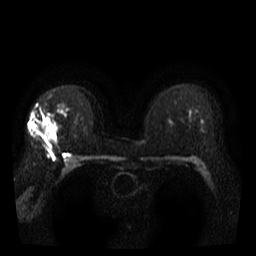
Breast MRI, one axial slice. Diffusion-weighted series; image 2 of 4 stored at this slice position (different b-values; order by instance number). 3 T. 5 mm slice thickness. 256 × 256 image matrix, field of view 300 × 300 mm. Female patient.
Outlined on this slice (expert manual segmentation):
- tumour on diffusion-weighted imaging: bounding box <41,116,61,134> (left, top, right, bottom; pixels)